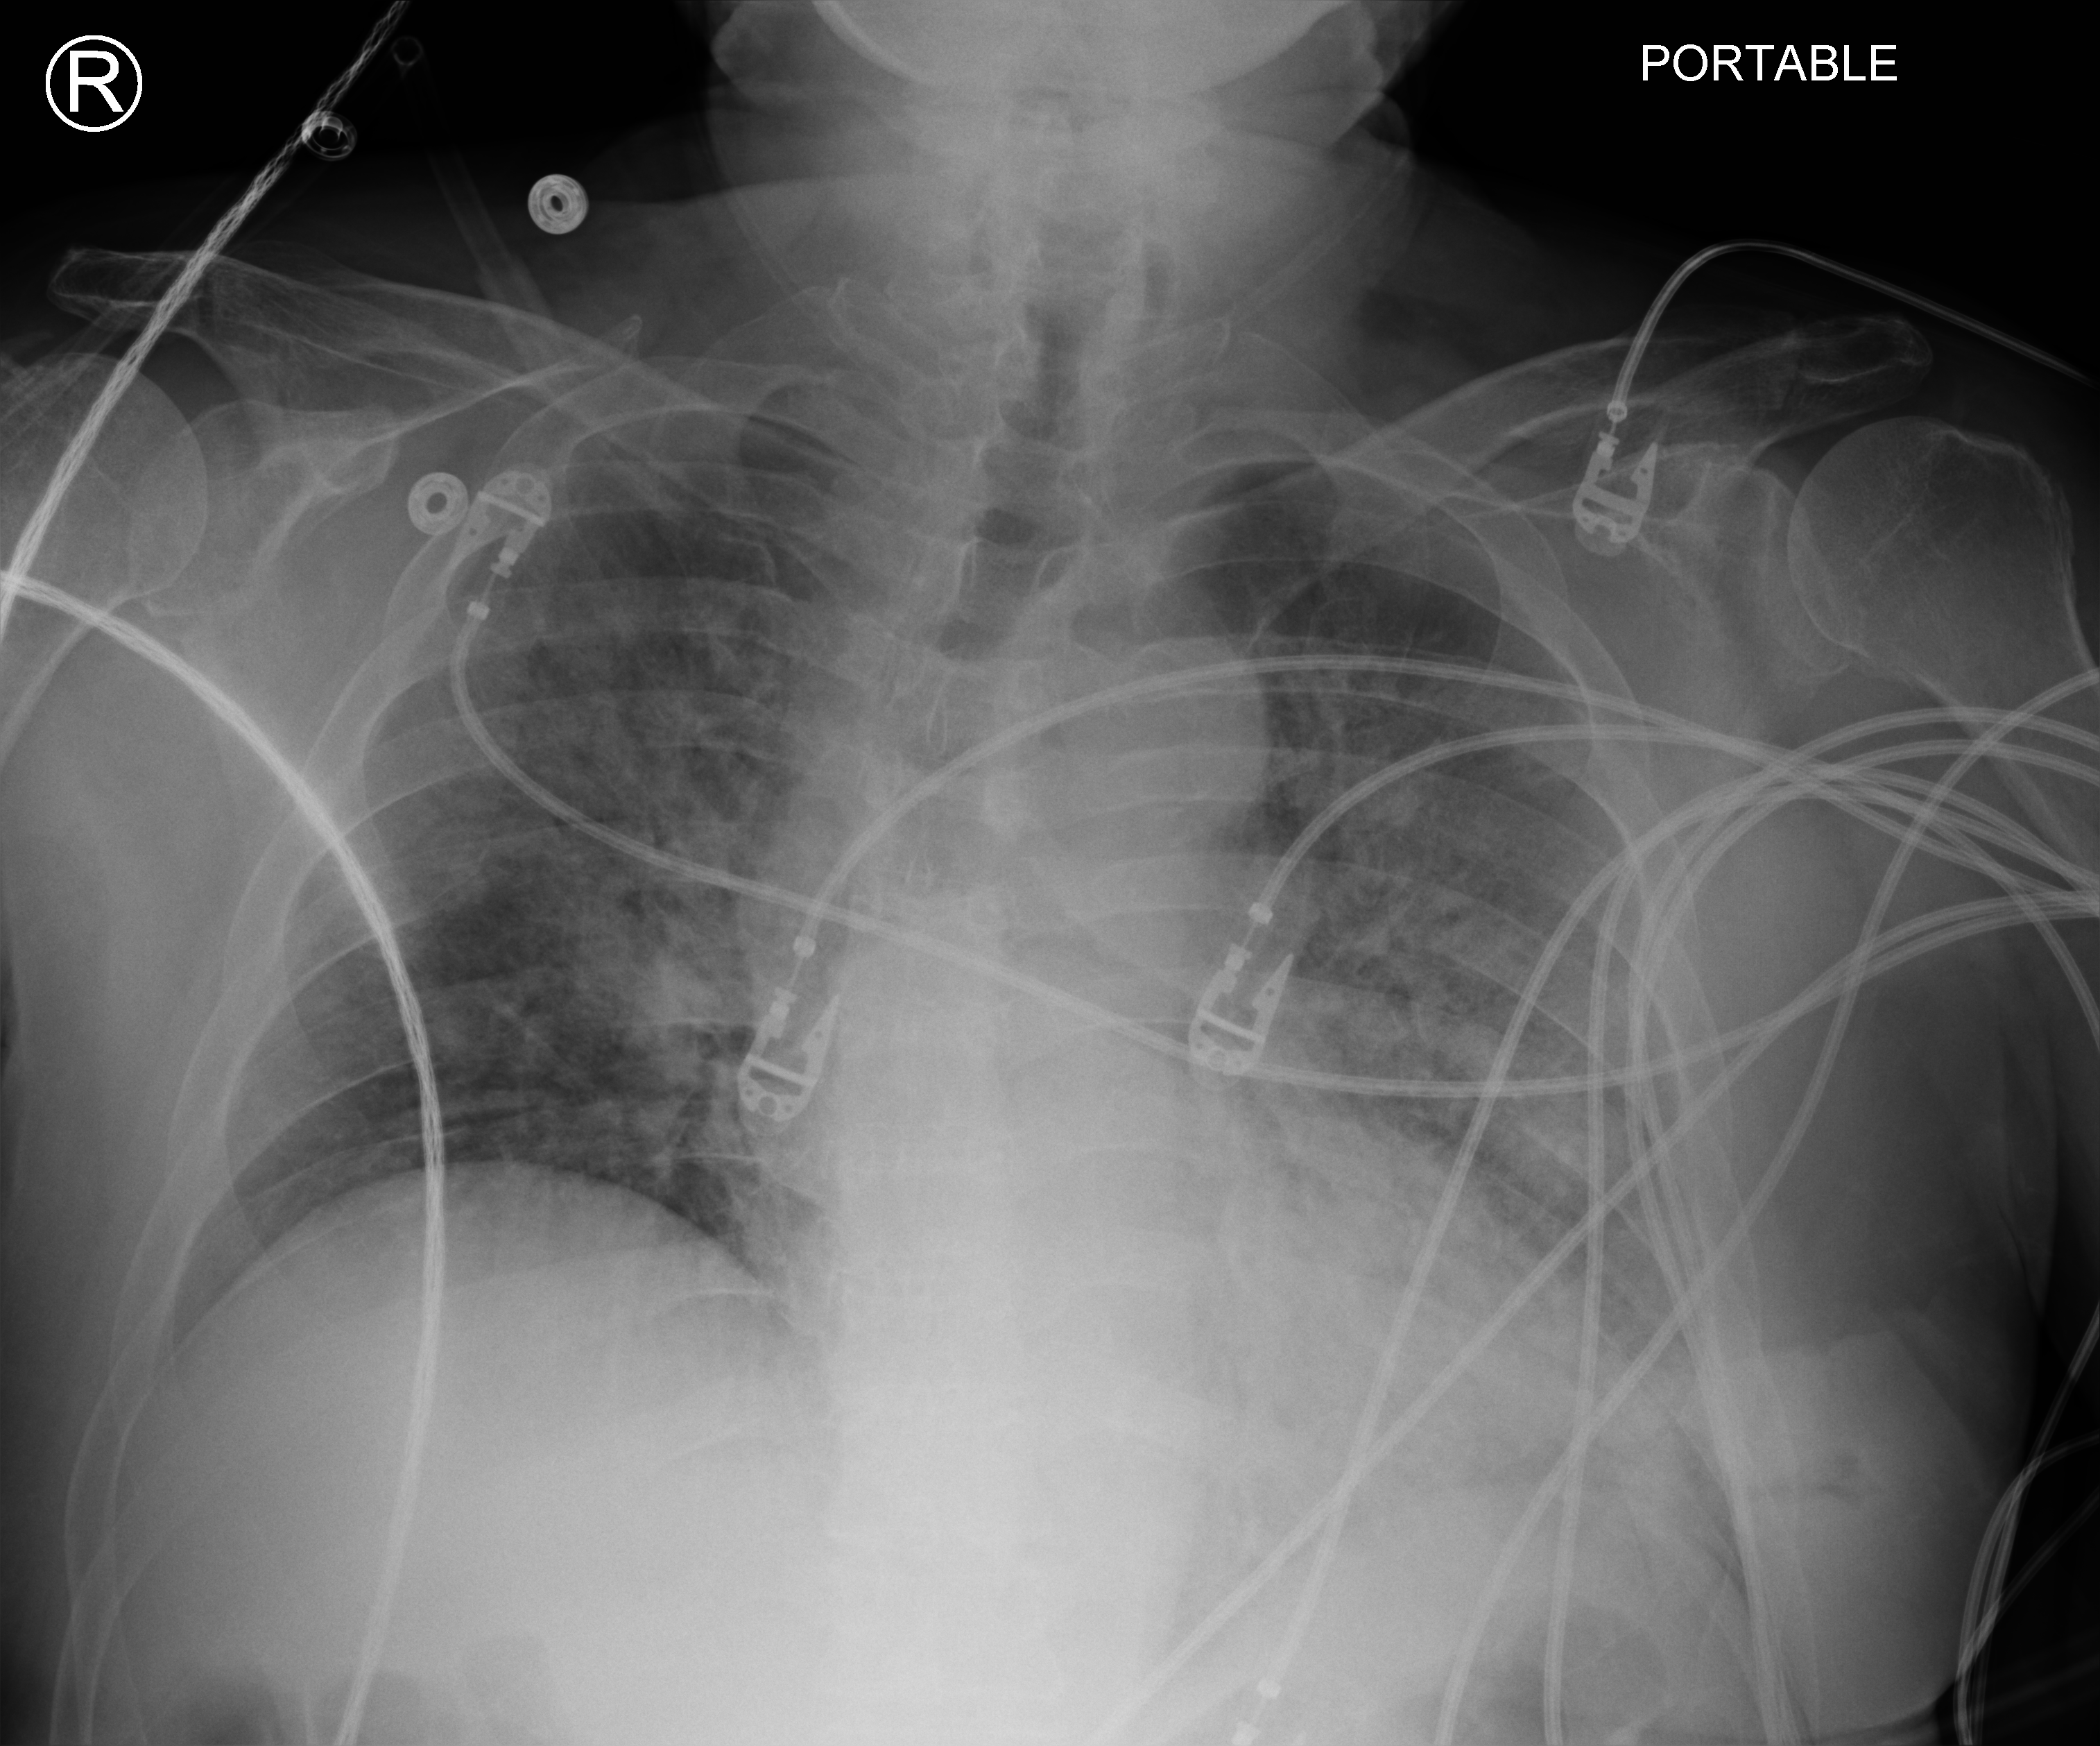
Bedside chest radiograph (computed radiography), anteroposterior (AP) projection. Male patient hospitalised with COVID-19, age 60–74 years.
Hospital-stay facts (about this admission, not read from this image; timing relative to this image not recorded): mechanically ventilated during this hospital stay: yes; admitted to intensive care during this hospital stay: yes.